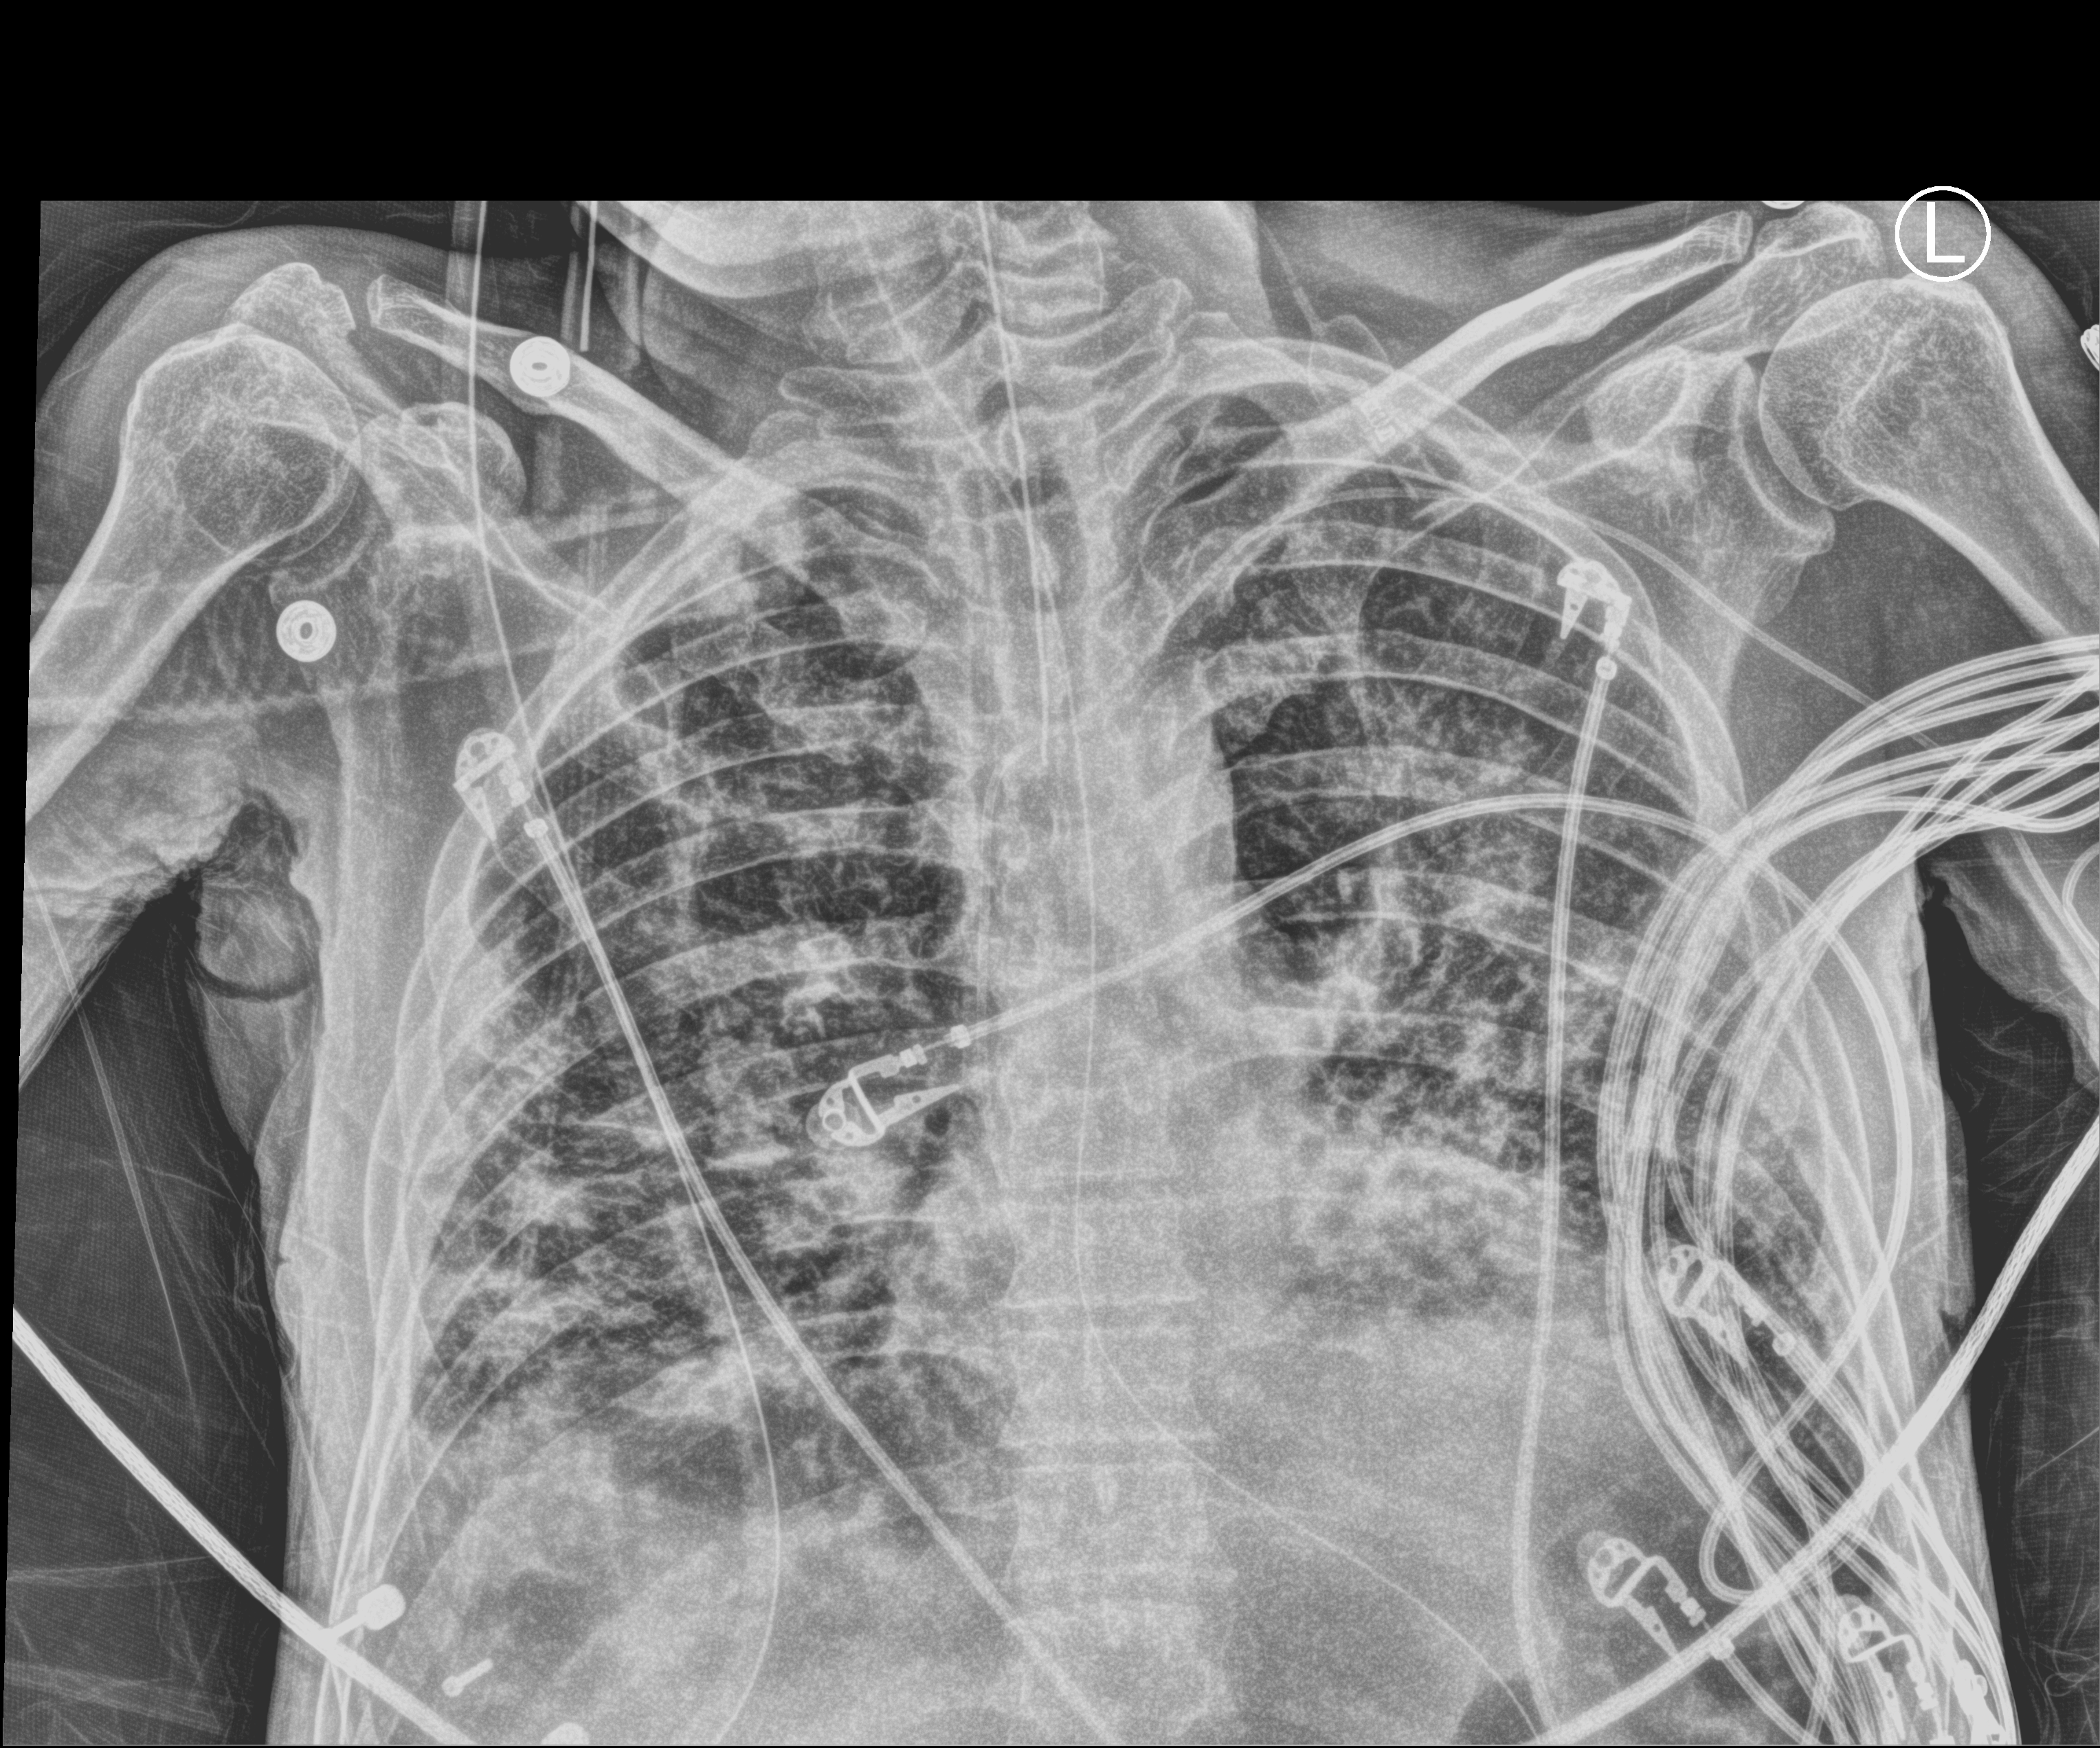
Bedside chest radiograph (computed radiography); anteroposterior (AP) projection. Patient hospitalised with COVID-19; male, aged 18–59 years.
From the hospital-stay record, not from the radiograph (when in the stay this image was taken is not recorded):
- admitted to intensive care during this hospital stay: yes